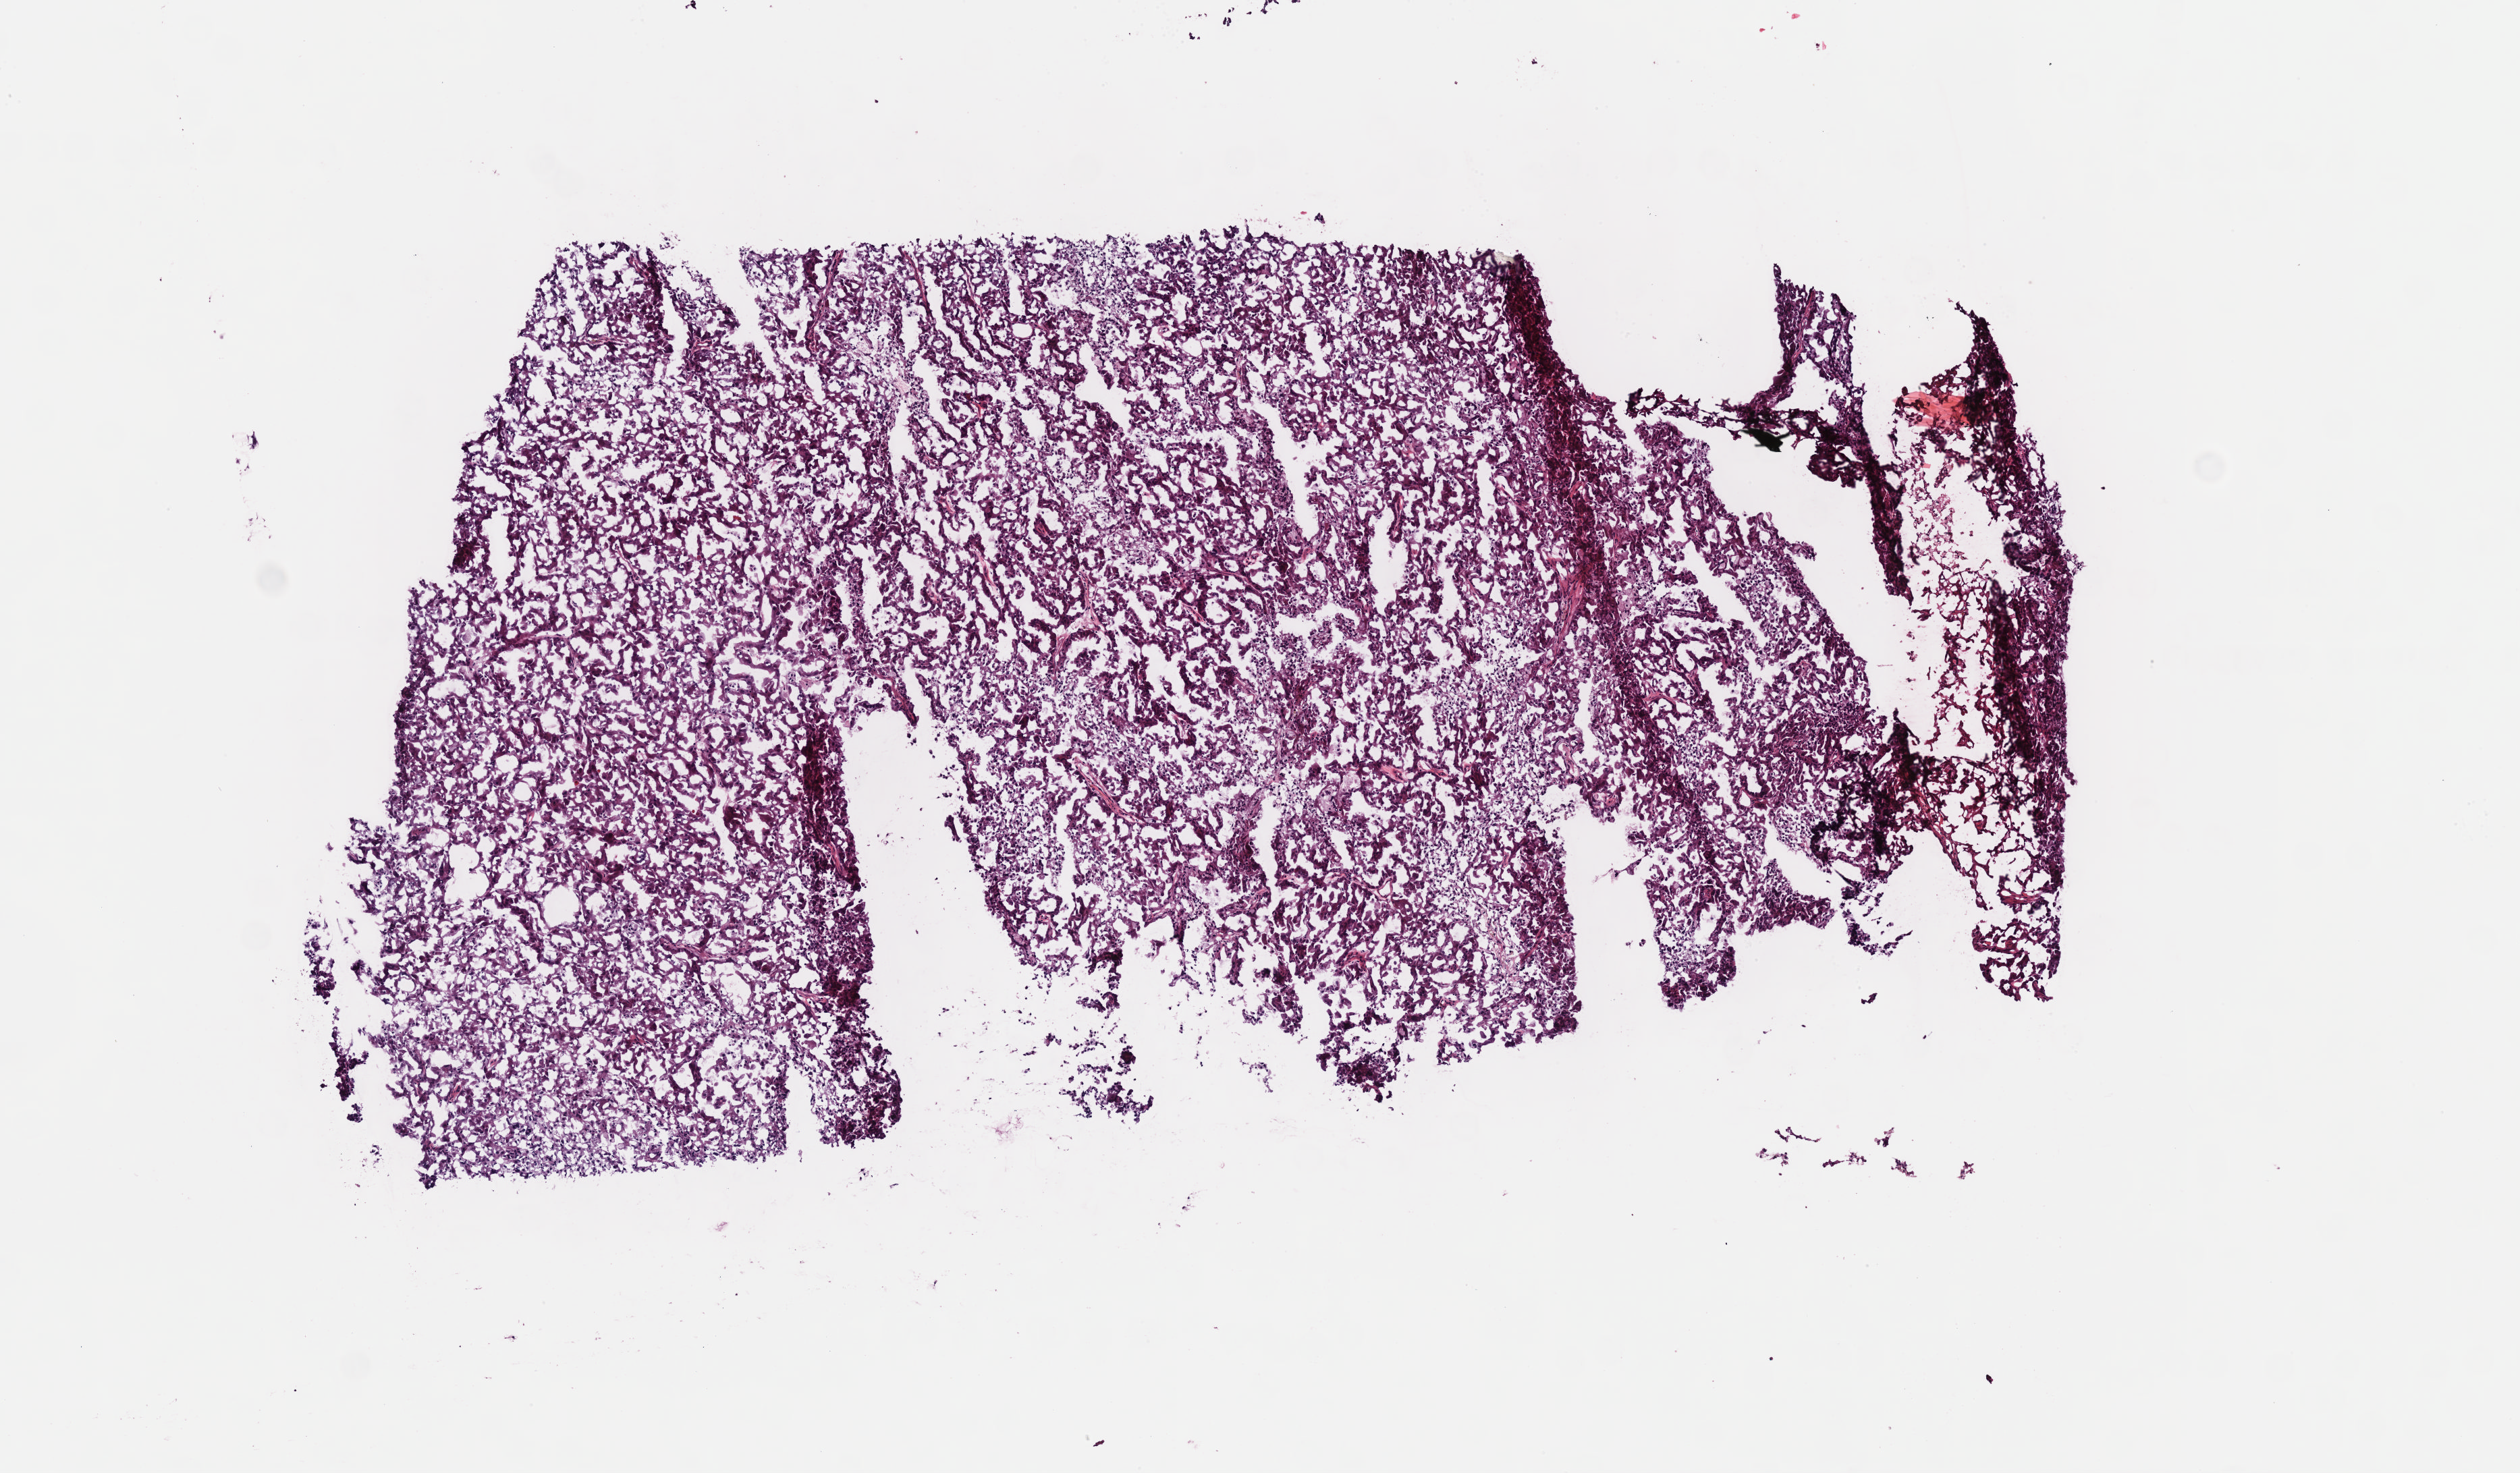
H&E whole-slide image — low-resolution overview of the scanned area, about 7.6 x 4.4 mm. Frozen section from the top of the tissue portion. Kidney, primary tumour sample. Patient: male, age at initial diagnosis 81 years. Composition of this section per pathologist review: tumour cells 70%, tumour nuclei 80%, normal cells 0%, stromal cells 30%, necrosis 0%. Inflammatory infiltration, as recorded: lymphocyte infiltration 0%, monocyte infiltration 0%, neutrophil infiltration 0%.
* histologic diagnosis: Papillary adenocarcinoma, NOS
* TNM: T3a N0 M0
* AJCC pathologic stage: III
* laterality: left